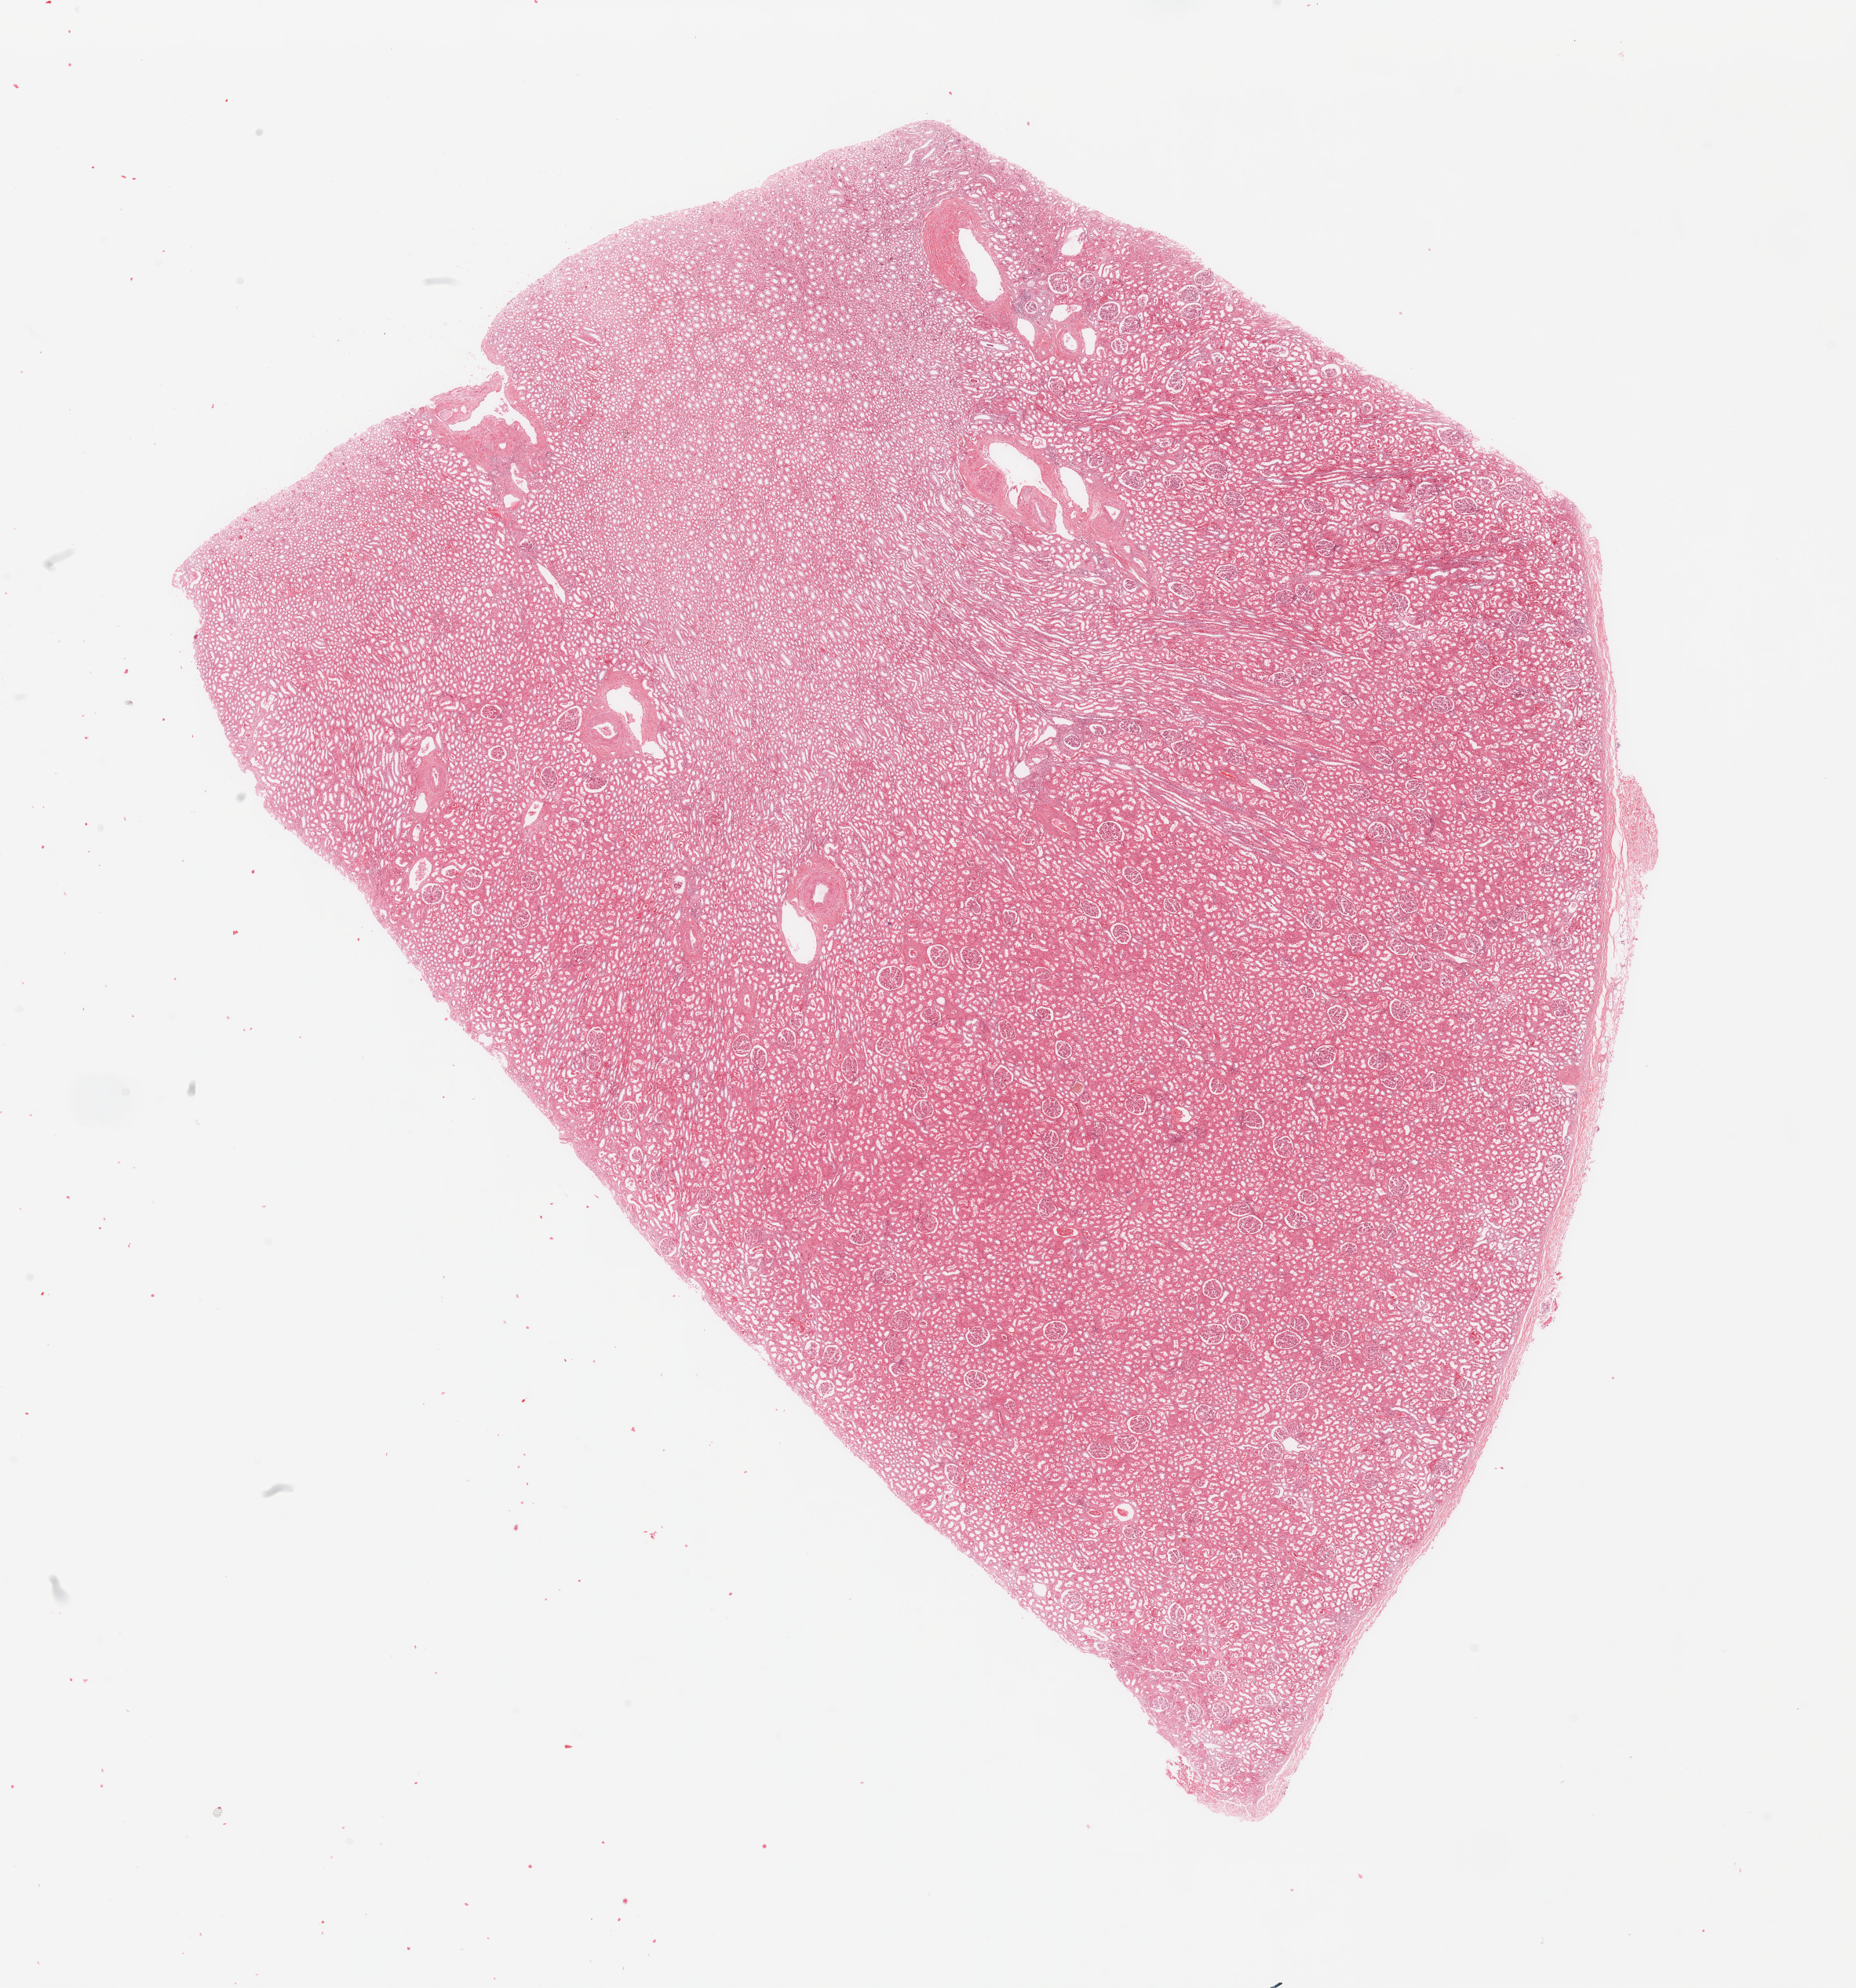
Whole-slide histology image, Hematoxylin and eosin (H&E) stained, a low-resolution overview of the entire scanned area, about 18.7 x 20.0 mm. Normal (non-tumour) tissue sample, sampled site: kidney. Patient: male, age 47 years.
• this section: normal (non-tumour) tissue from the same patient
• patient diagnosis: Renal cell carcinoma, NOS